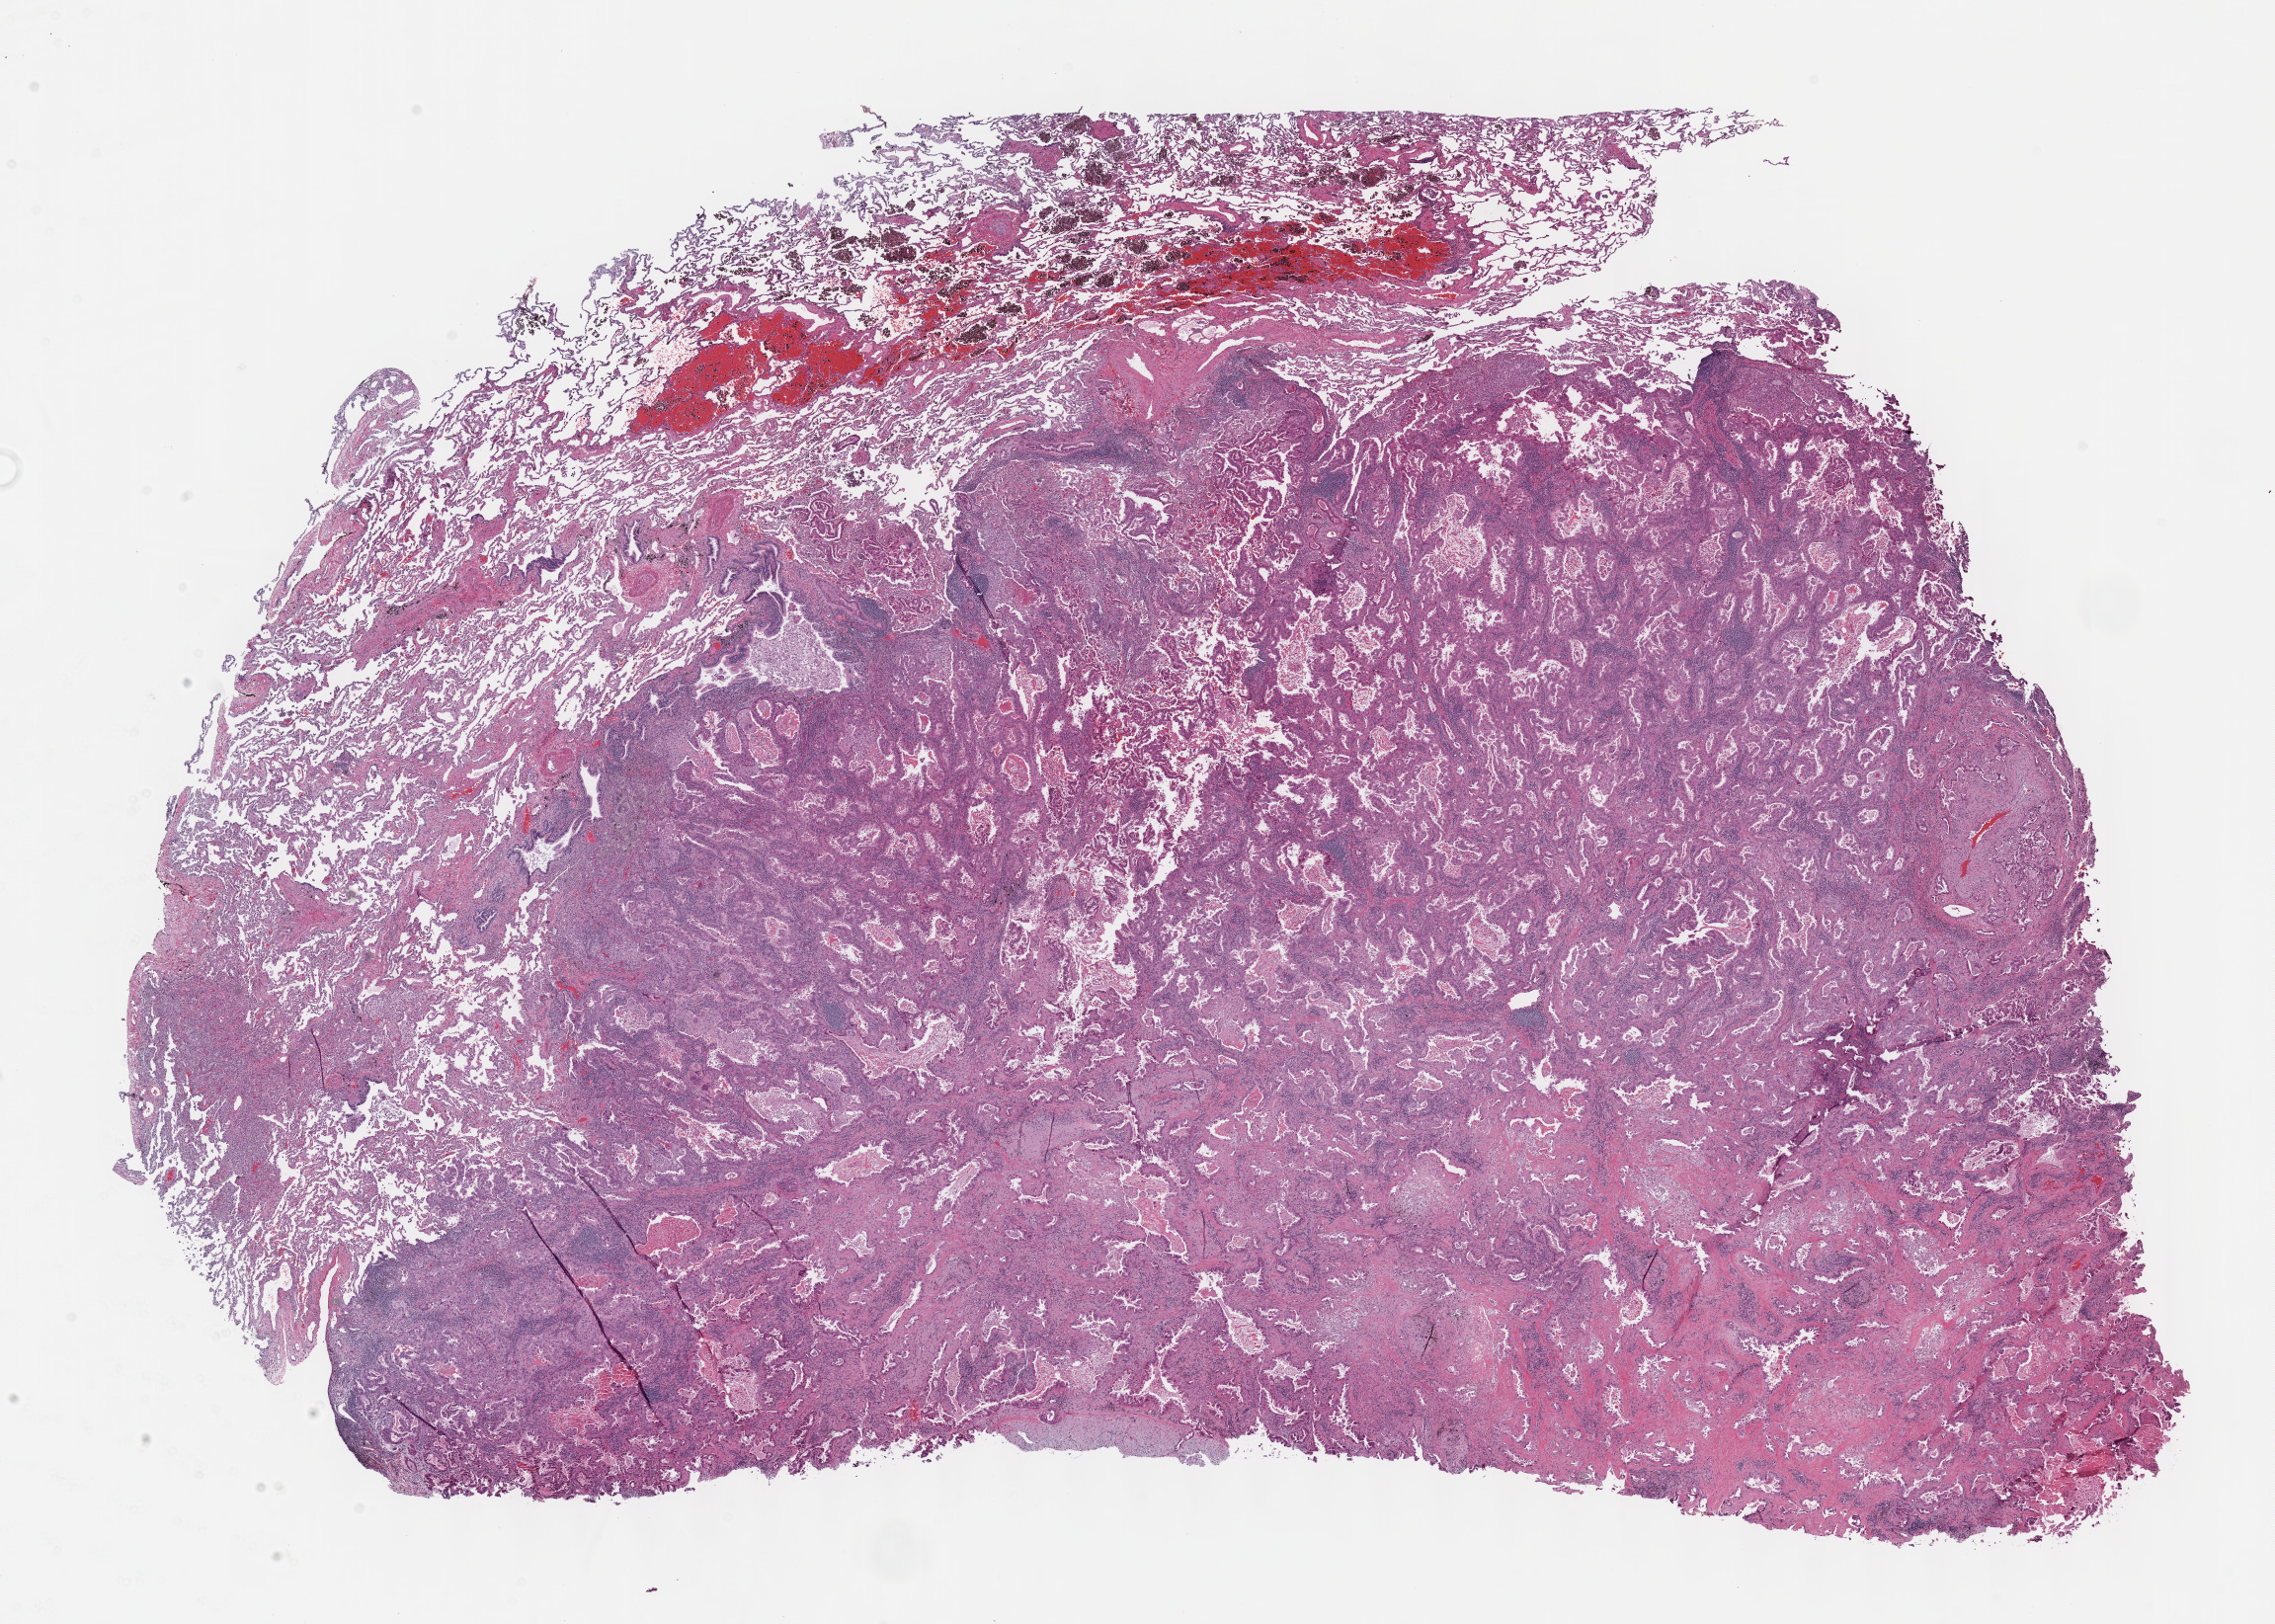
Whole-slide histology image, H&E — a low-resolution overview of the entire scanned area, about 18.6 x 13.3 mm (acquisition: 40x scan). FFPE section. Lung, primary tumour sample. Male patient; age at initial diagnosis 53 years.
AJCC pathologic stage: IIB (5th edition). Pathologic diagnosis: Adenocarcinoma, NOS (upper lobe, lung).